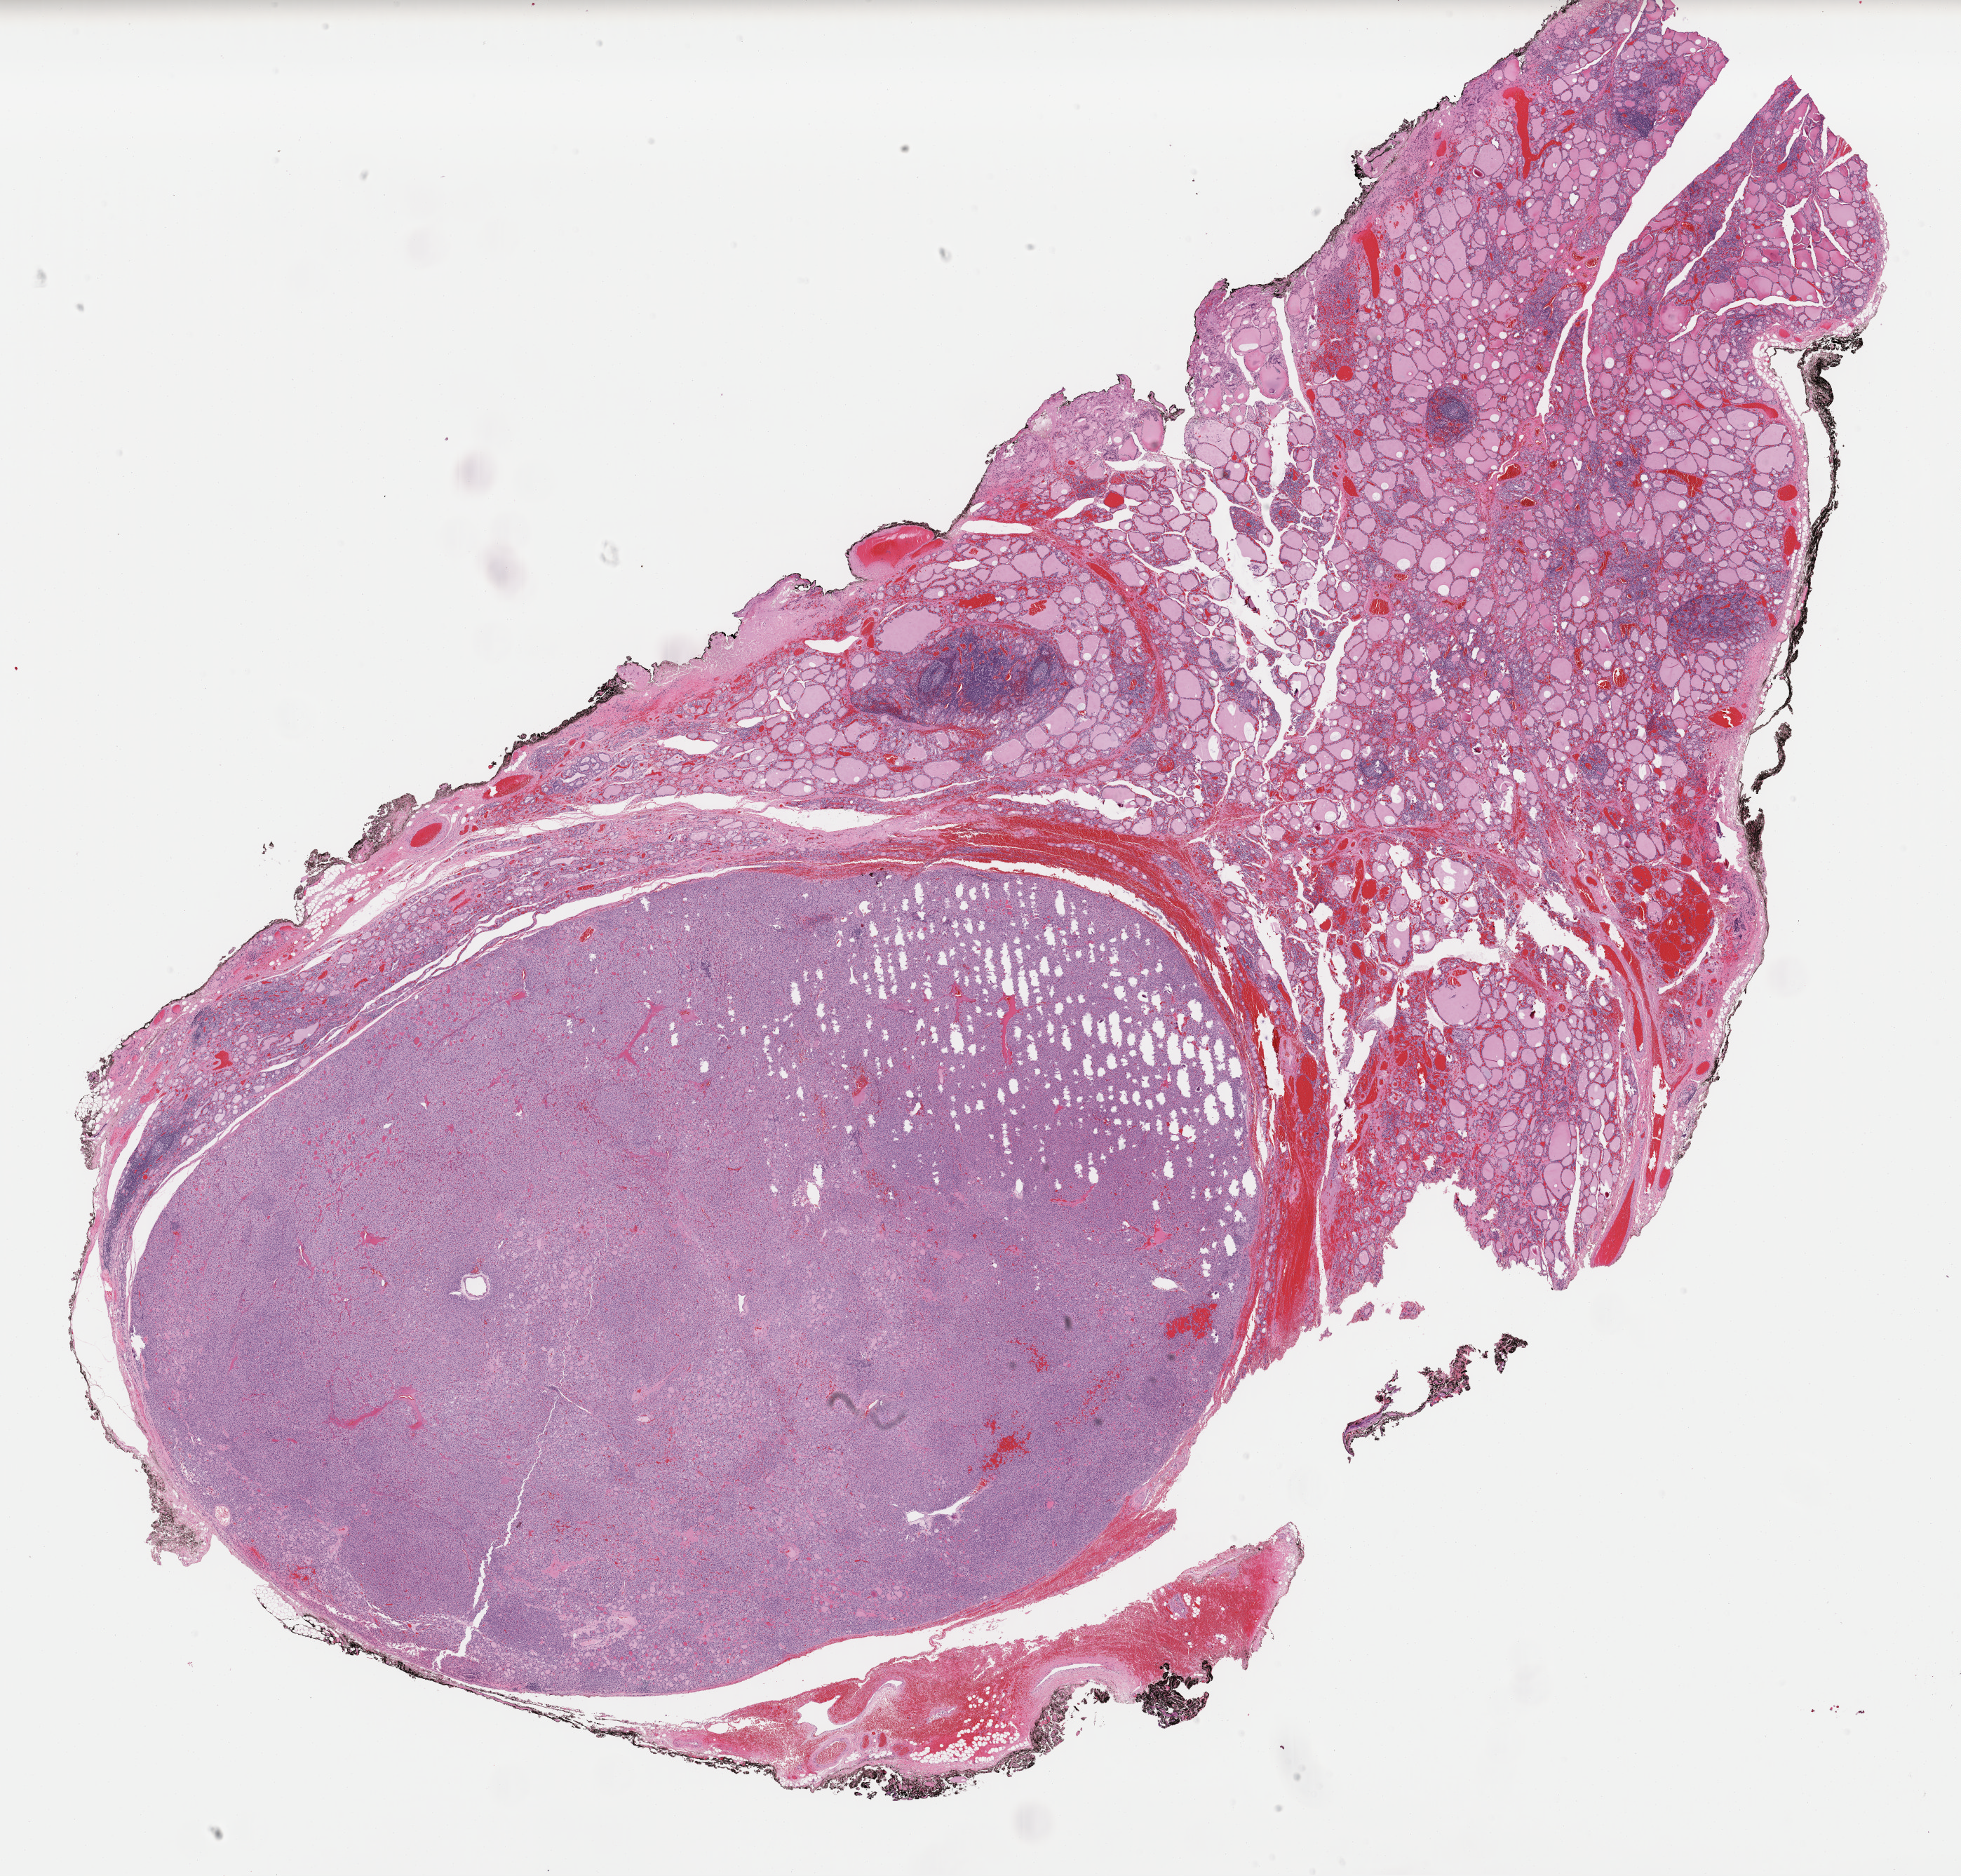
Whole-slide histology image, H&E-stained — a low-resolution overview of the entire scanned area, about 22.1 x 21.1 mm. Formalin-fixed paraffin-embedded (FFPE) diagnostic section. Primary tumour sample from the thyroid. Female patient; age at initial diagnosis 37 years.
TNM: T1b N0 MX. Lymph nodes positive (case pathology): 1 of 20 examined. Histologic diagnosis: Papillary carcinoma, follicular variant (thyroid gland). Laterality: bilateral. AJCC pathologic stage: I.